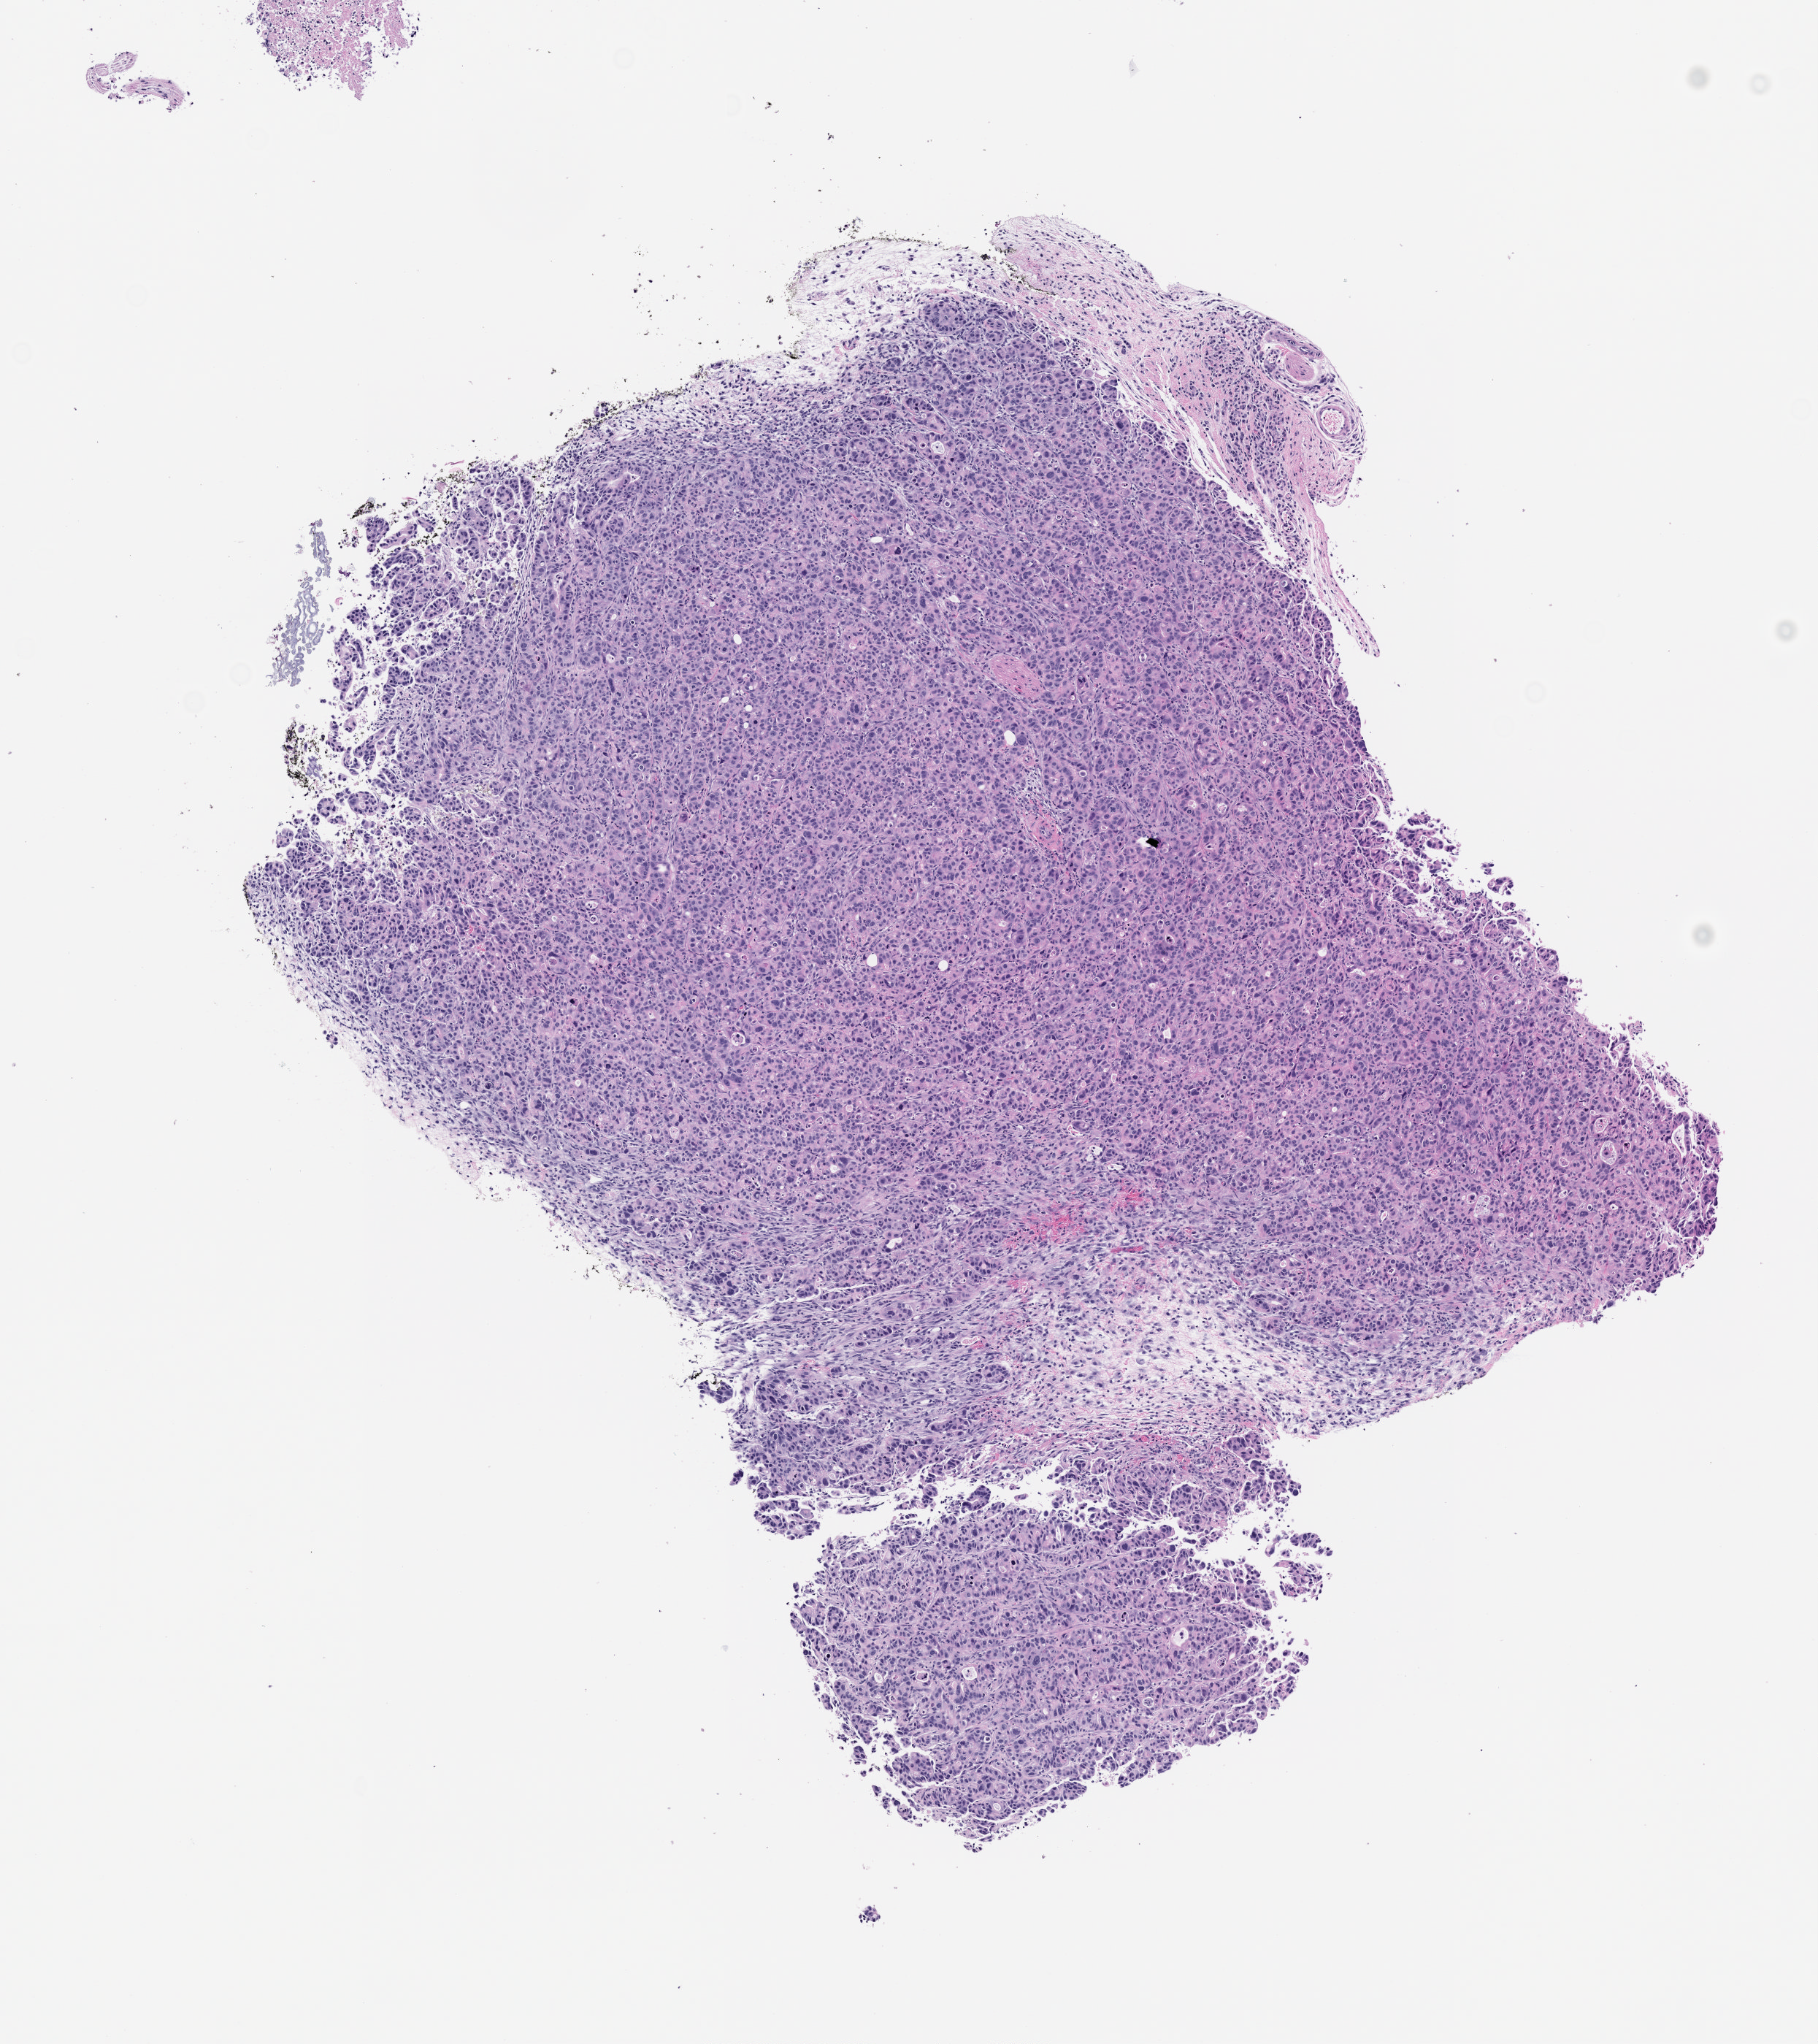
Haematoxylin and eosin whole-slide image of a patient-derived xenograft (PDX) tumor grown in a mouse, passage 1, low-resolution overview of the scanned area, about 5.0 x 5.6 mm. Formalin-fixed paraffin-embedded section. Tumor site category: pancreas.
* originating patient diagnosis: Pancreatic Adenocarcinoma